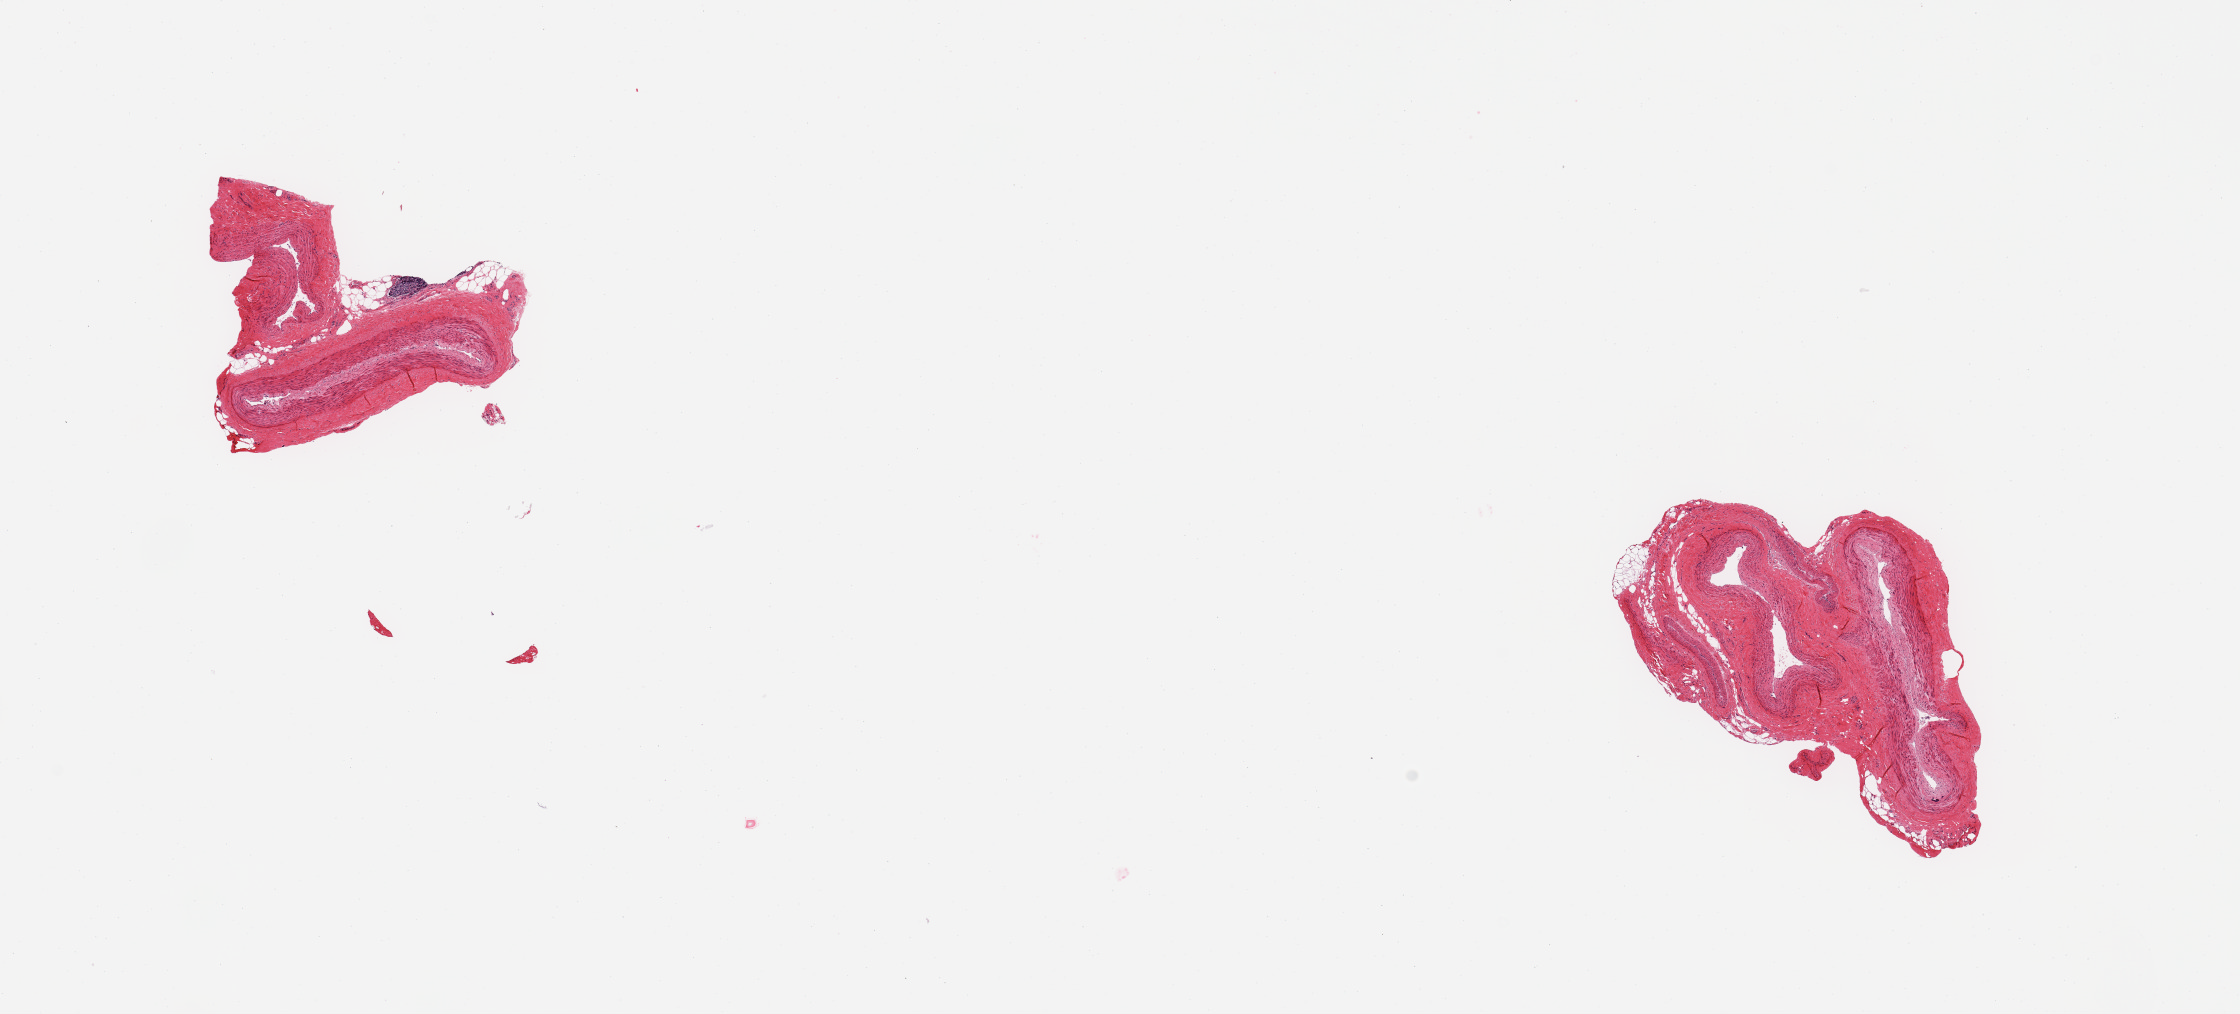
Whole-slide image, hematoxylin and eosin (H&E) stain — shown as a low-resolution overview of the whole scanned area (about 17.7 x 8.0 mm); PAXgene-fixed, paraffin-embedded tissue; target tissue: tibial artery; tissue donor sample. Donor: female.
Reviewer comment on this tissue sample: 2 pieces; from 30-50% attached vein/fat.